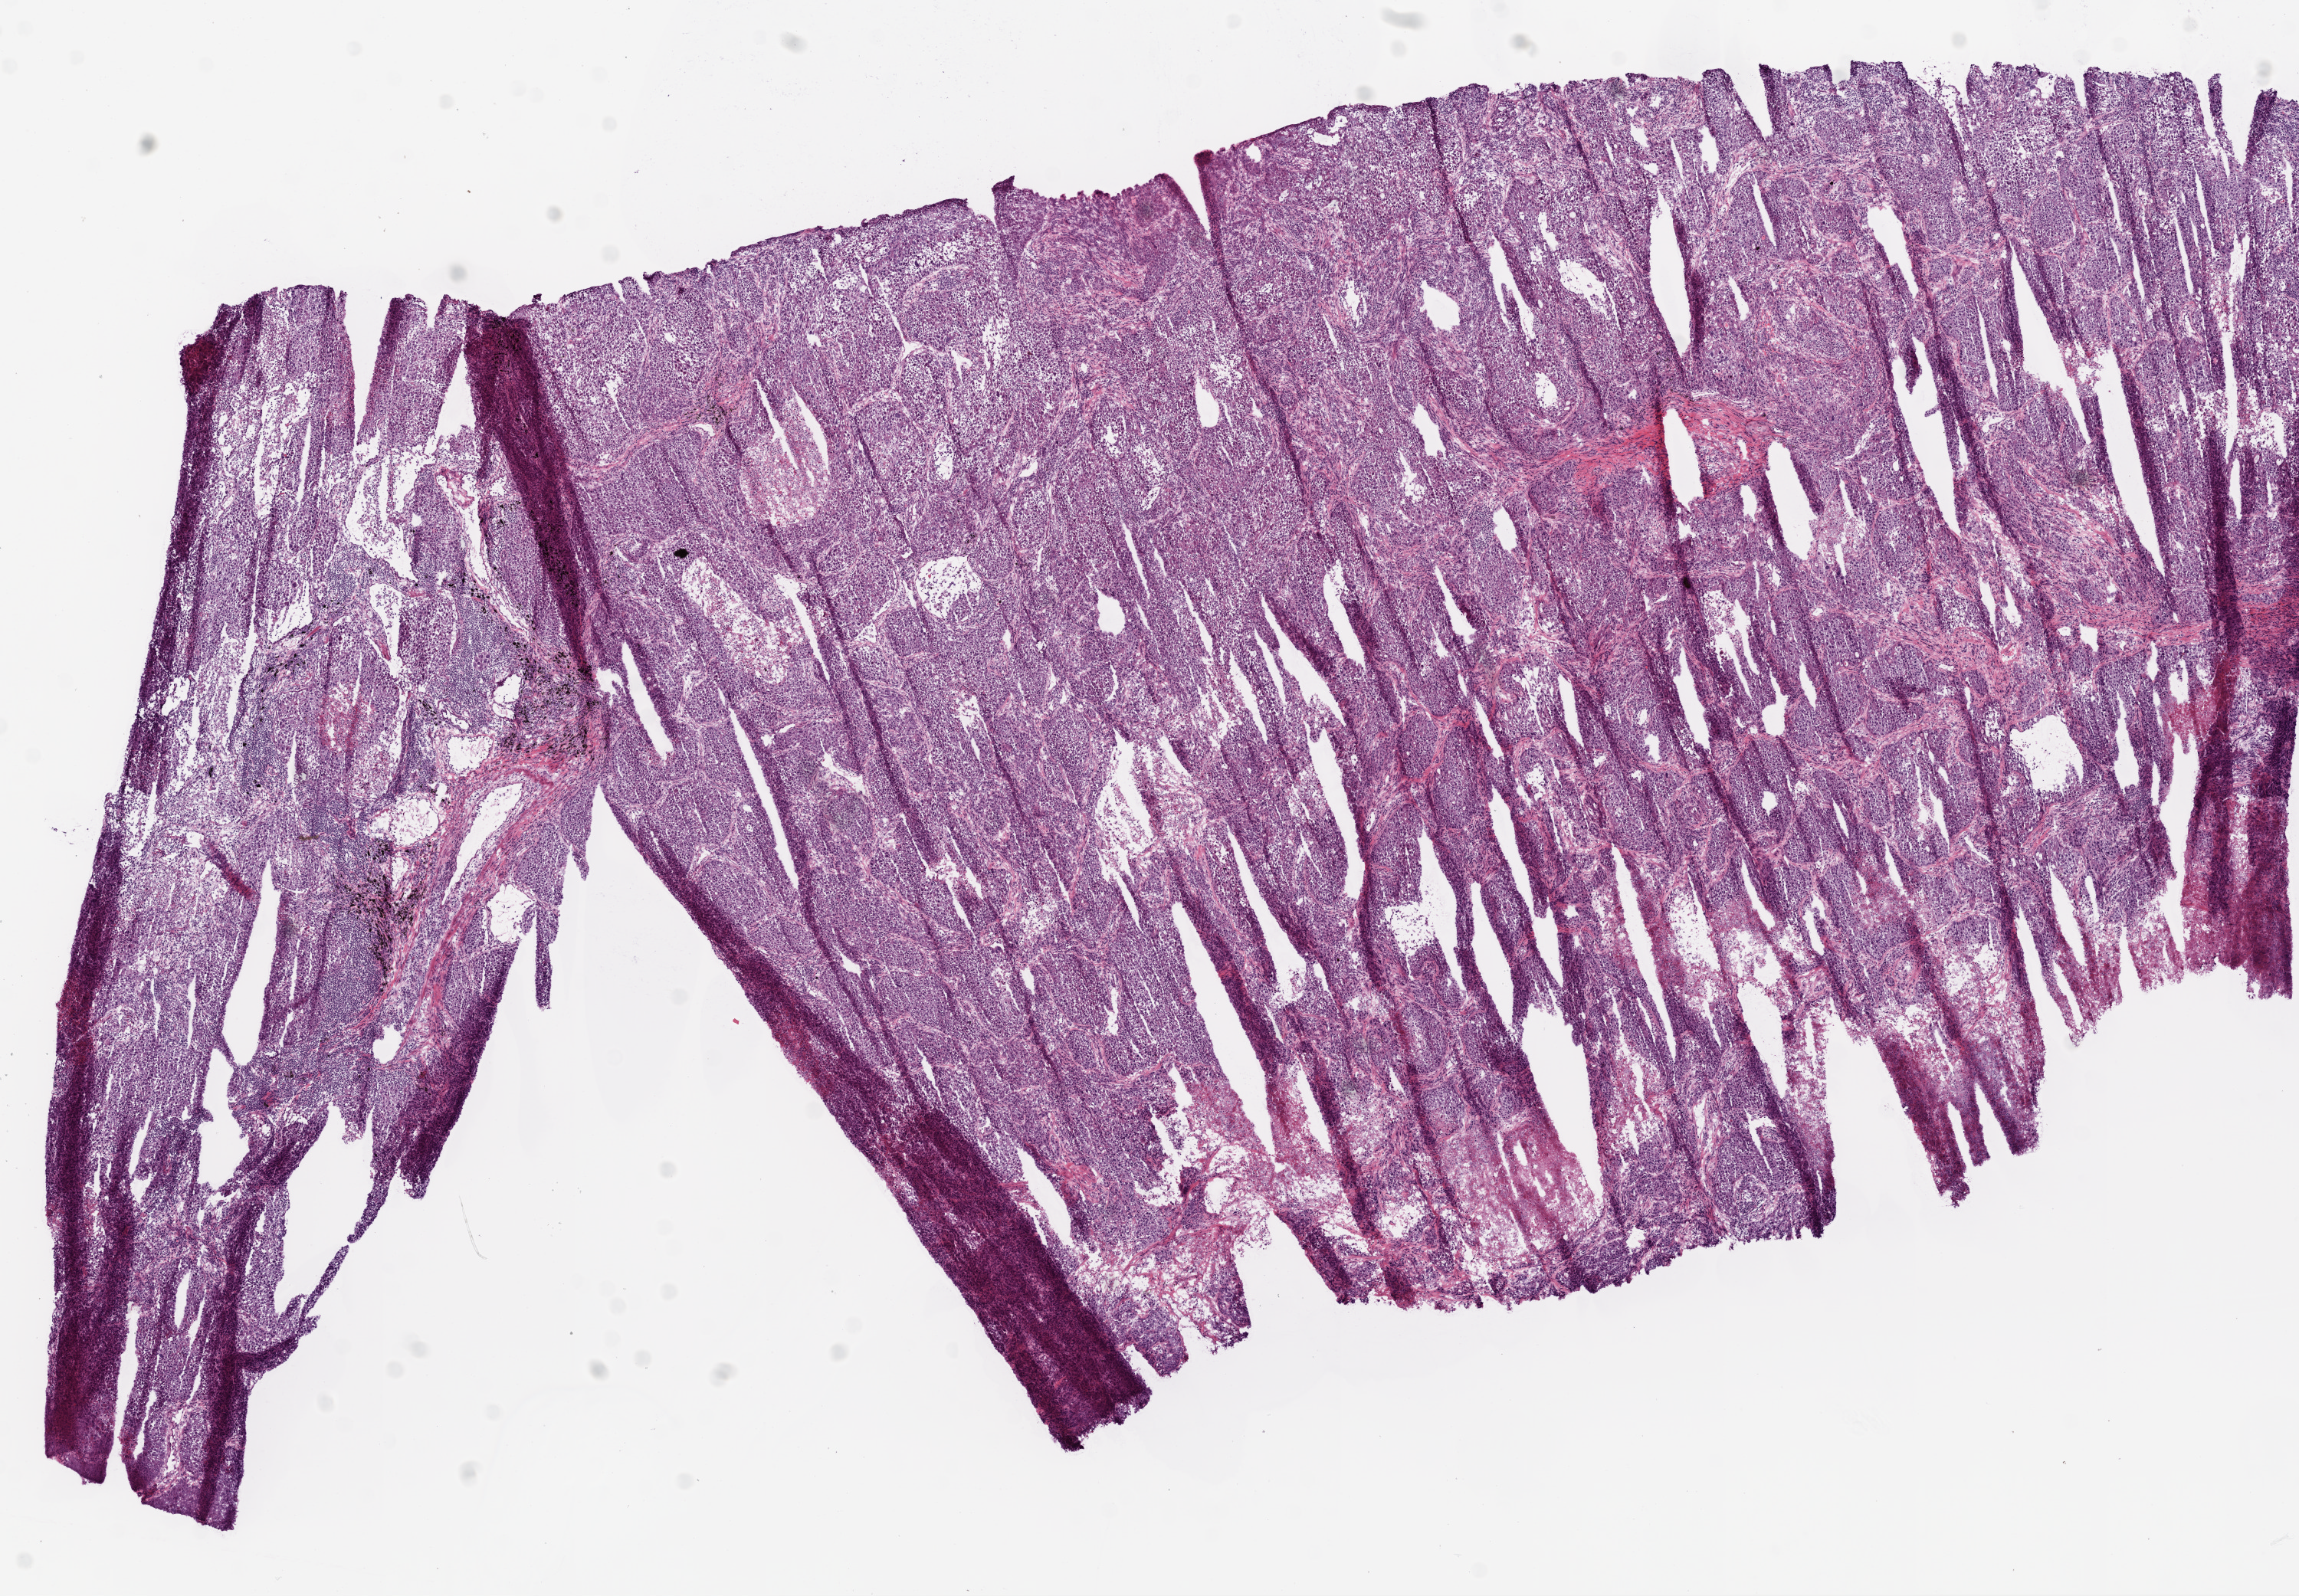
Whole-slide histology image, H&E-stained, a low-resolution overview of the entire scanned area, about 12.0 x 8.4 mm (acquisition: 20x scan). Frozen section. Lung, primary tumour sample. Male, age 65 years at initial diagnosis. Pathologist review of this section (percent, as recorded): tumour cells 72%, tumour nuclei 70%, normal cells 3%, stromal cells 5%, necrosis 20%. Infiltration values recorded for this section: lymphocyte infiltration 22%, monocyte infiltration 0%, neutrophil infiltration 0%.
Diagnosis: Squamous cell carcinoma, NOS. AJCC pathologic stage: IB (6th edition).